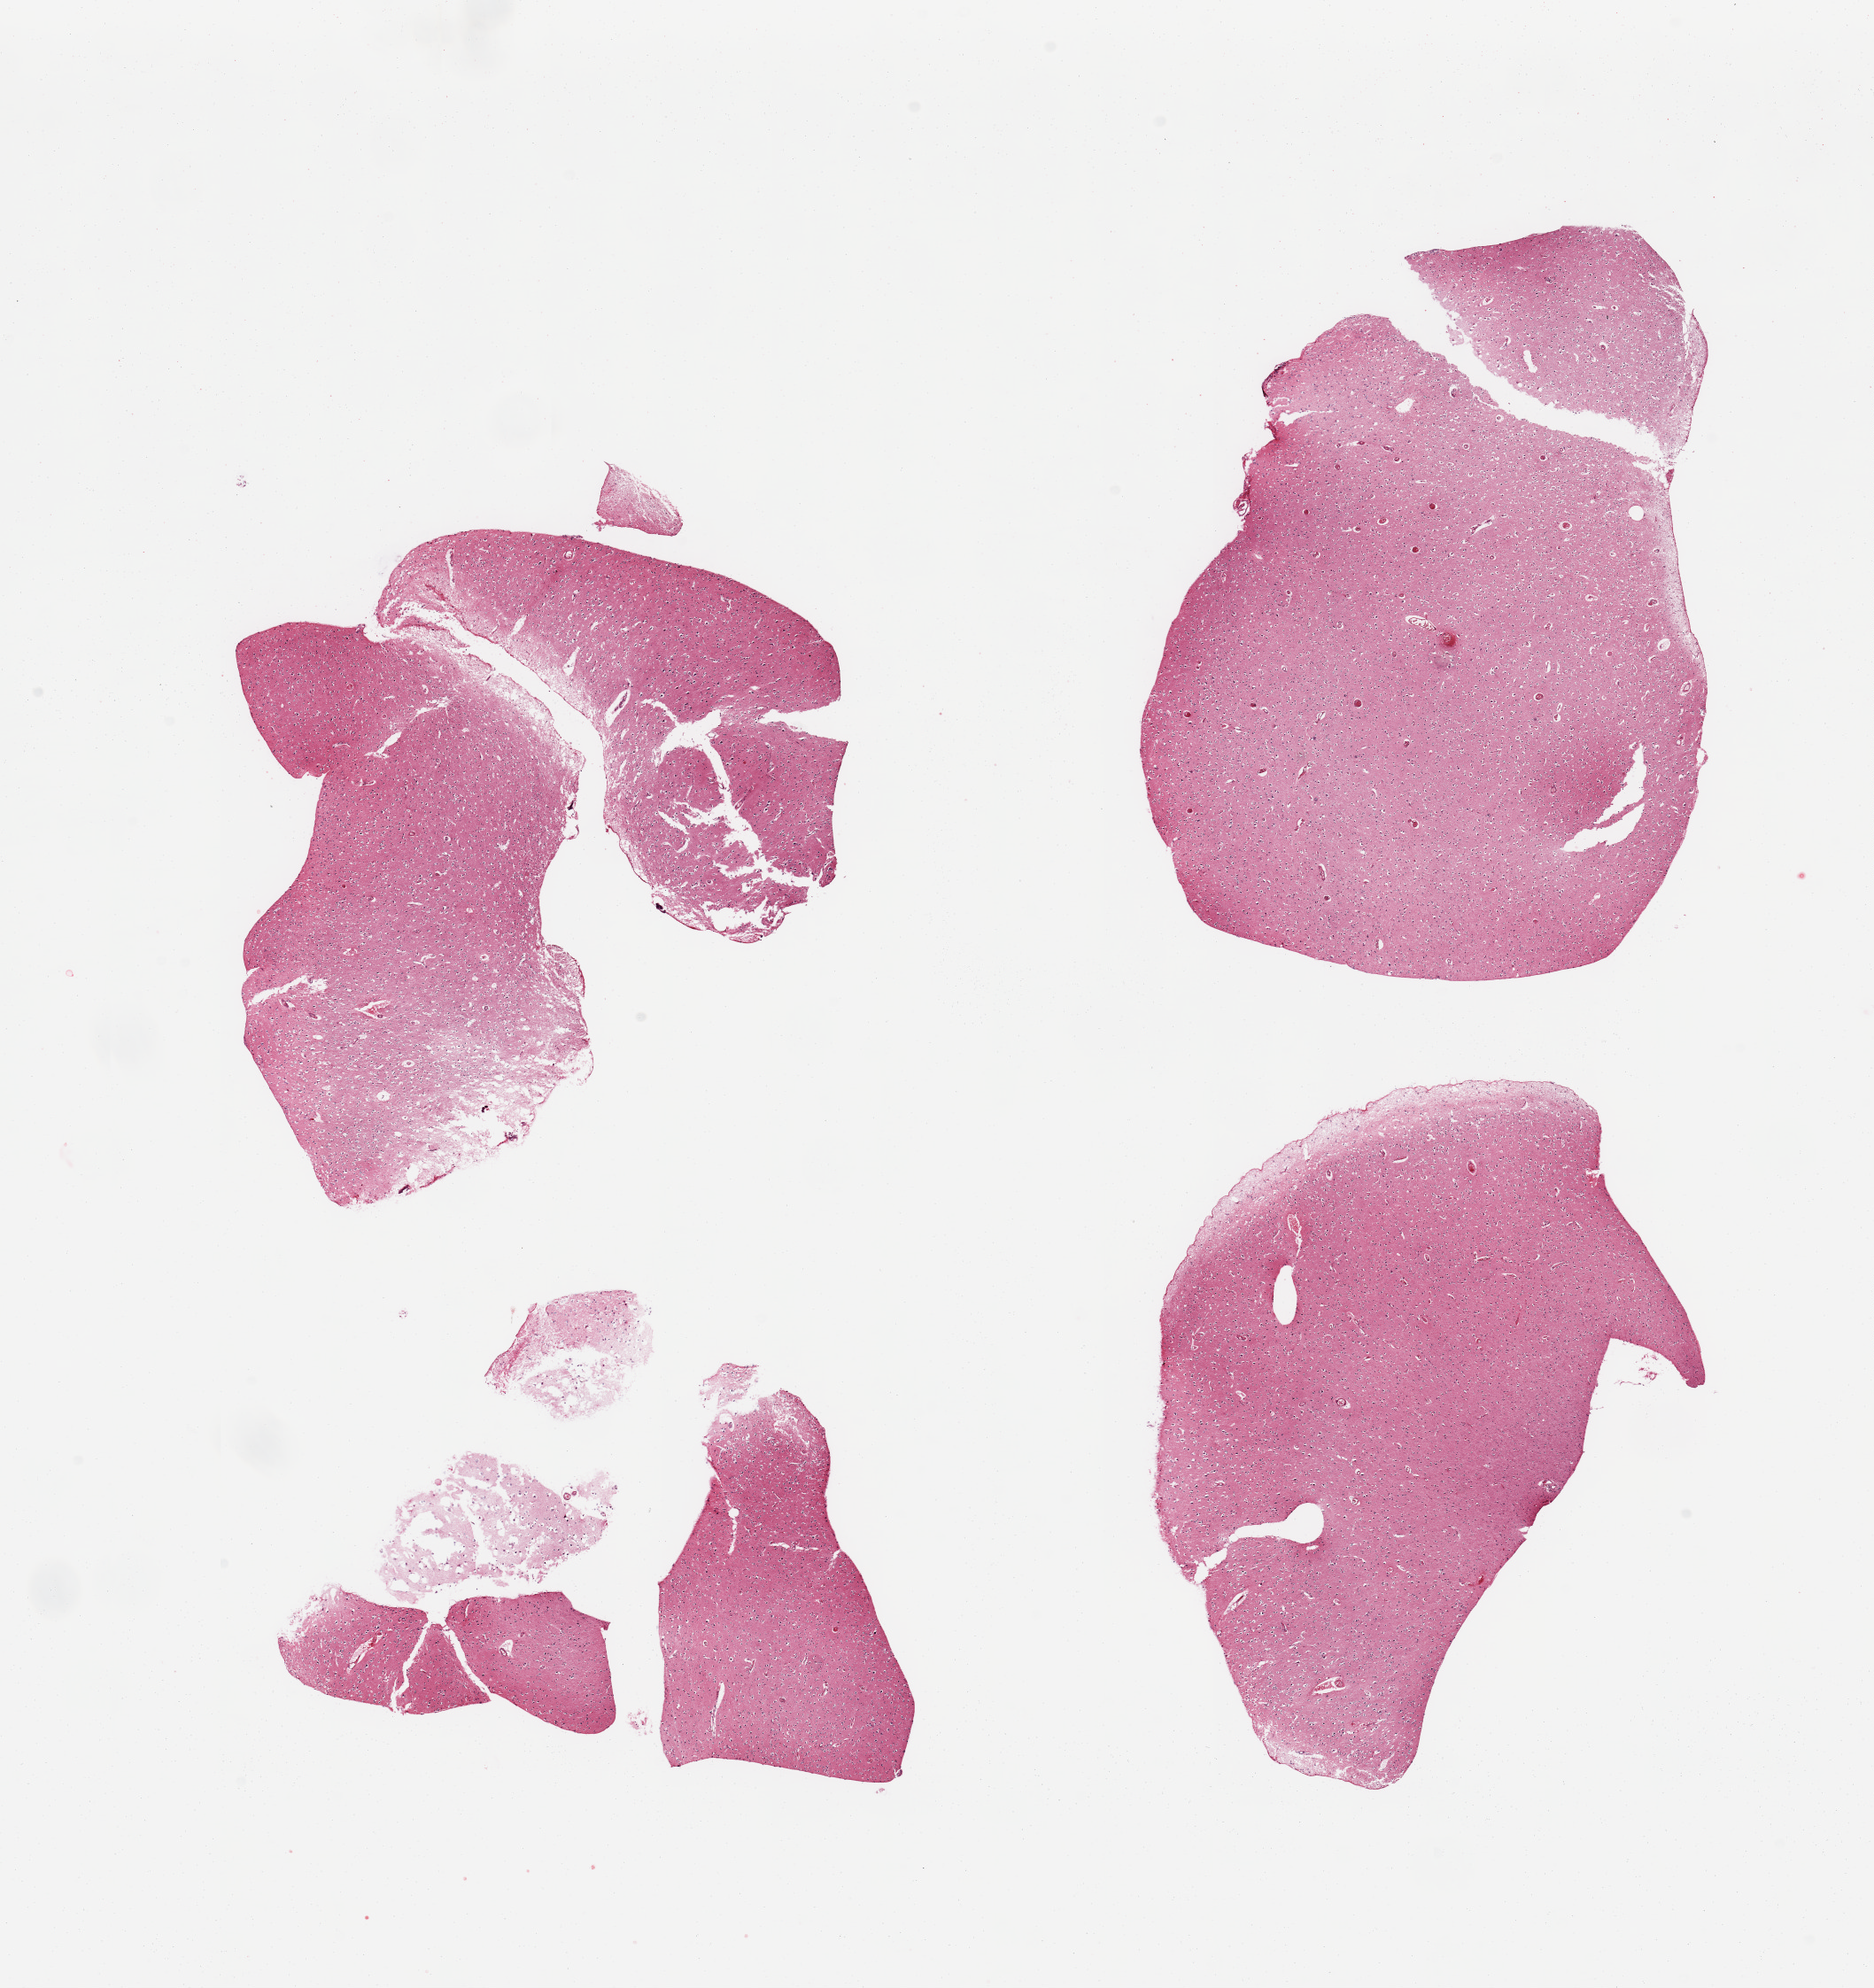
H&E whole-slide image, brightfield, shown as a low-resolution overview of the whole scanned area (about 16.7 x 17.8 mm), PAXgene-fixed, paraffin-embedded tissue, sampled site (target tissue): cerebral cortex, tissue donor sample. Male donor.
- reviewer comment on this tissue sample: 4 pieces, fragmented, no abnormalites